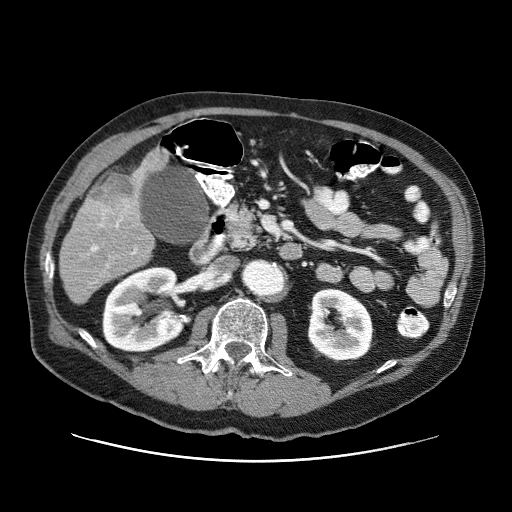
Contrast-enhanced abdominal CT (liver protocol), one axial slice; slice 21 of 87 in the series (ordered by position); 120 kVp; one of 3 acquisitions stored at this slice position; soft-tissue window (W 400 / L 40 HU); 2.5 mm slice thickness; 512 × 512 image matrix, field of view 400 × 400 mm. Case-level facts recorded for this patient, not image findings: diagnosis: hepatocellular carcinoma (patient treated with transarterial chemoembolisation; whether this scan precedes or follows treatment is not stated here); TNM stage (as recorded): Stage-IIIA; Child-Pugh class: A; tumour differentiation: well differentiated; tumour size: 6 cm.
Outlined on this slice (semi-automatic segmentation, software-assisted and operator-edited):
- liver parenchyma outside the tumour (the mass and vessels are separate outlines, so this box may not span the whole liver): box from (x=60, y=148) to (x=168, y=304) px
- mass: (x=84, y=172)–(x=139, y=224)
- liver vessels: (x=91, y=220)–(x=137, y=267)